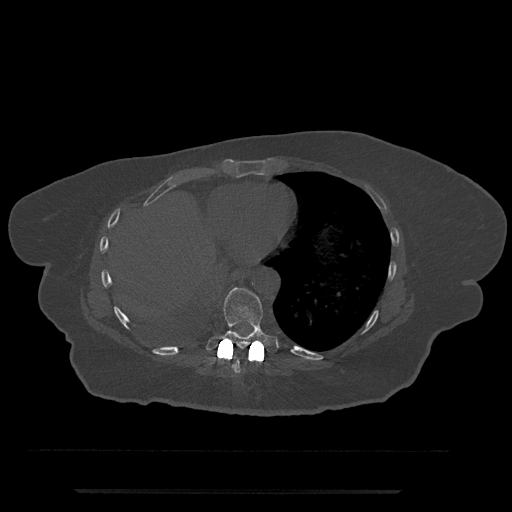
CT including the spine, one axial slice. Slice 343 of 797 in the series (ordered by position). Reconstruction kernel Br40s/3. Bone window (W 1800 / L 400 HU). 512 × 512 image matrix, field of view 440 × 440 mm. Patient: female, 51 years. From the clinical record (not read from this slice): primary cancer: neuro; vertebrae with lytic lesions (as recorded): T8.
Structures marked on this image (semi-automatic segmentation, software-assisted and operator-edited):
- T8 vertebra: bounding box [x1, y1, x2, y2] px = [234, 350, 250, 374]
- T9 vertebra: [206, 287, 277, 353]